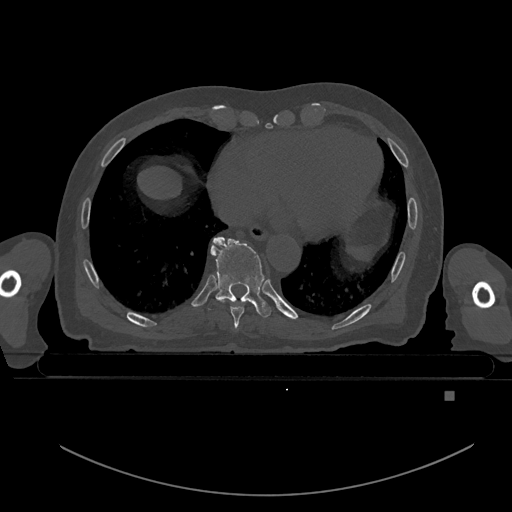
CT including the spine, one axial slice. Position 166 of 969 along the scan axis. Bone window (W 1800 / L 400 HU). 0.5 mm slice thickness. 512 × 512 image matrix. Patient: male, 82 years. From the clinical record (not read from this slice): primary cancer: prostate.
Annotated regions visible in this slice (semi-automatic segmentation, software-assisted and operator-edited):
- T8 vertebra: bounding box [x1, y1, x2, y2] px = [215, 298, 249, 328]
- T9 vertebra: [210, 236, 271, 318]